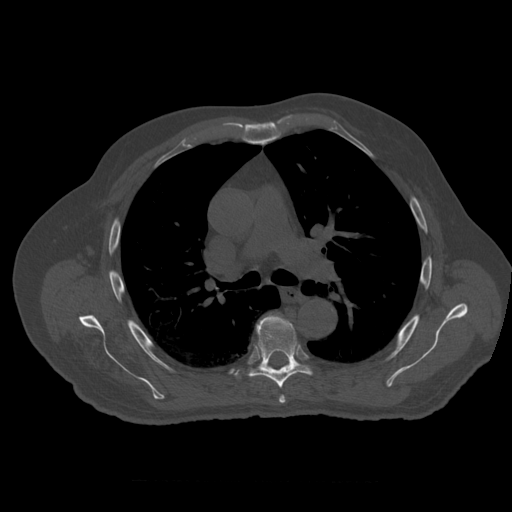
CT including the spine, one axial slice; position 384 of 399 along the scan axis; bone window (W 1800 / L 400 HU); 512 × 512 image matrix, field of view 407 × 407 mm. Patient age 73 years. Case-level facts recorded for this patient, not image findings: primary cancer: prostate.
Structures marked on this image (semi-automatically segmented with operator editing):
- T5 vertebra: bounding box (x1, y1, x2, y2) in pixels: (280, 396, 286, 404)
- T6 vertebra: (235, 315, 321, 389)